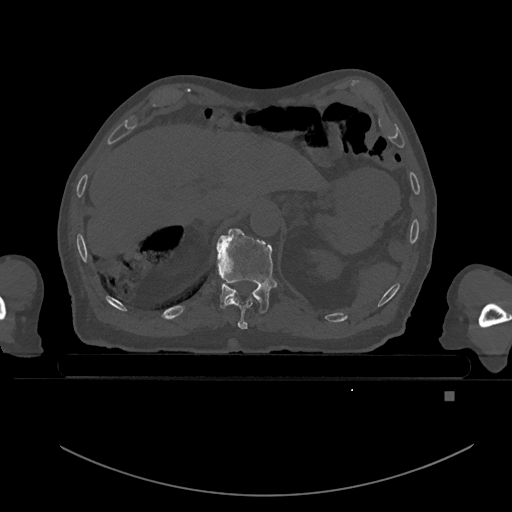
CT including the spine, one axial slice; slice 51 of 969 in the series (ordered by position); bone window (W 1800 / L 400 HU); 0.5 mm slice thickness; 512 × 512 image matrix, field of view 456 × 456 mm. Patient: male, 82 years. Case-level facts recorded for this patient, not image findings: primary cancer: prostate; vertebrae with lytic lesions (as recorded): T11, T9, T8, T2.
Outlined on this slice (semi-automatic segmentation, software-assisted and operator-edited):
- T10 vertebra: box from (x=226, y=296) to (x=255, y=330) px
- T11 vertebra: (x=216, y=228)–(x=276, y=313)